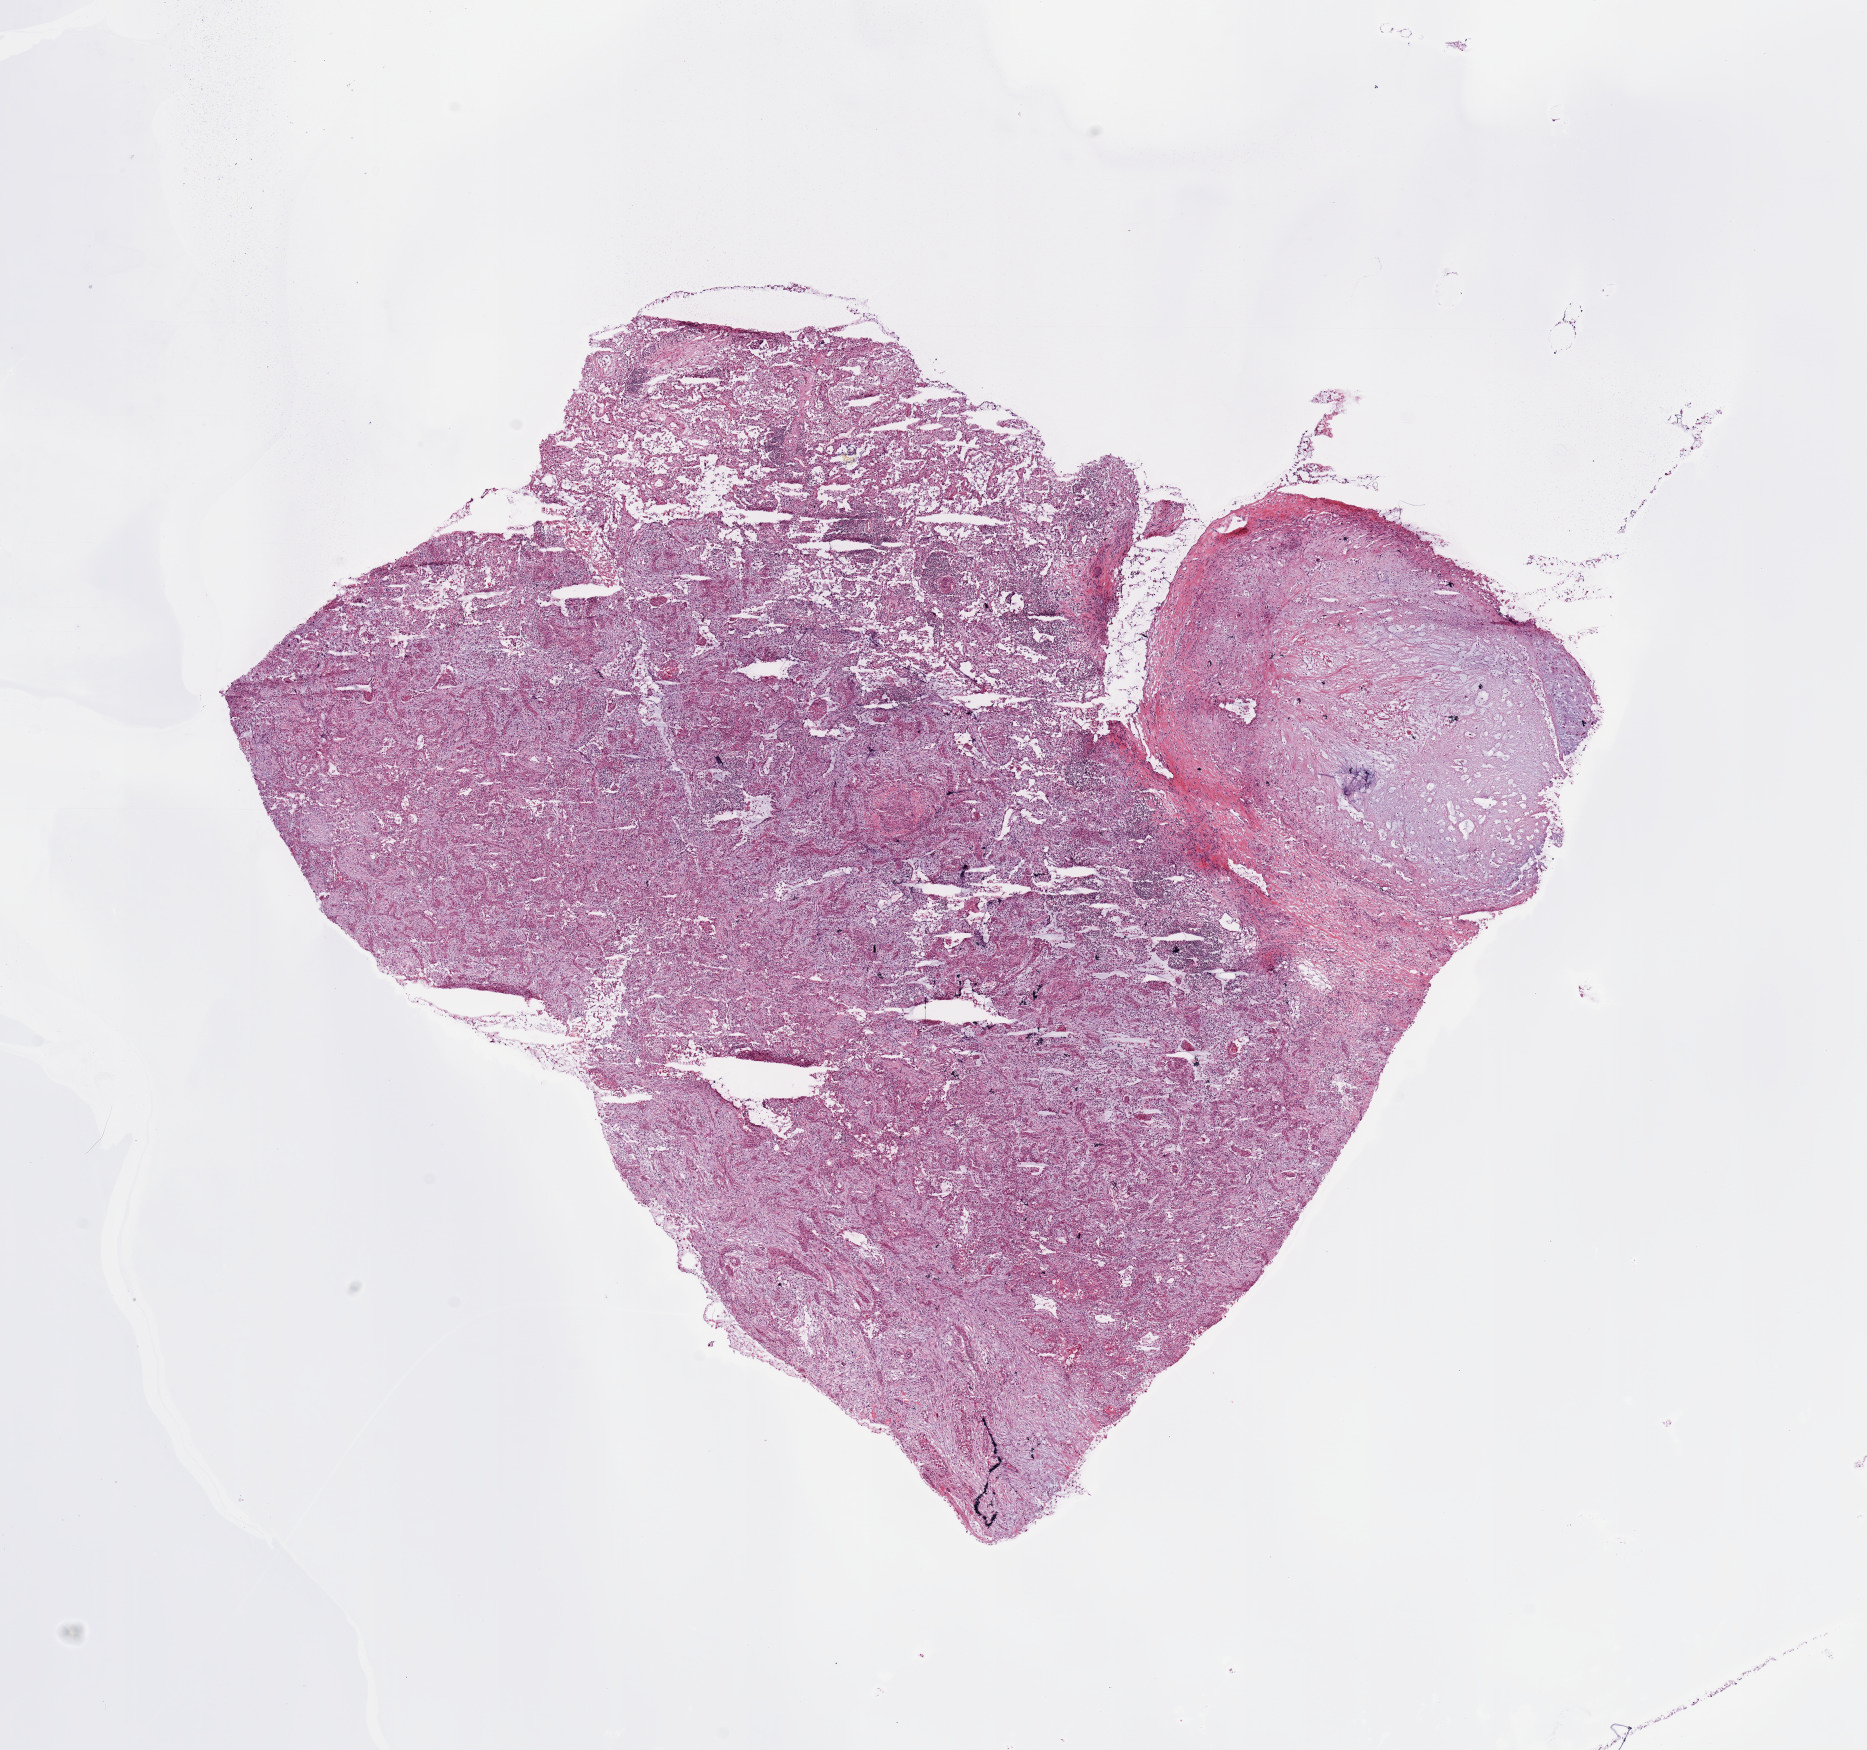
Whole-slide histology image, H&E — shown as a low-resolution overview of the whole scanned area (about 14.8 x 13.8 mm, acquisition: 20x scan), tumour tissue sample, lung. Patient: female, age 75 years.
- patient diagnosis (cohort enrolment): squamous cell carcinoma (lung)
- primary tumour site (as recorded): right upper lobe